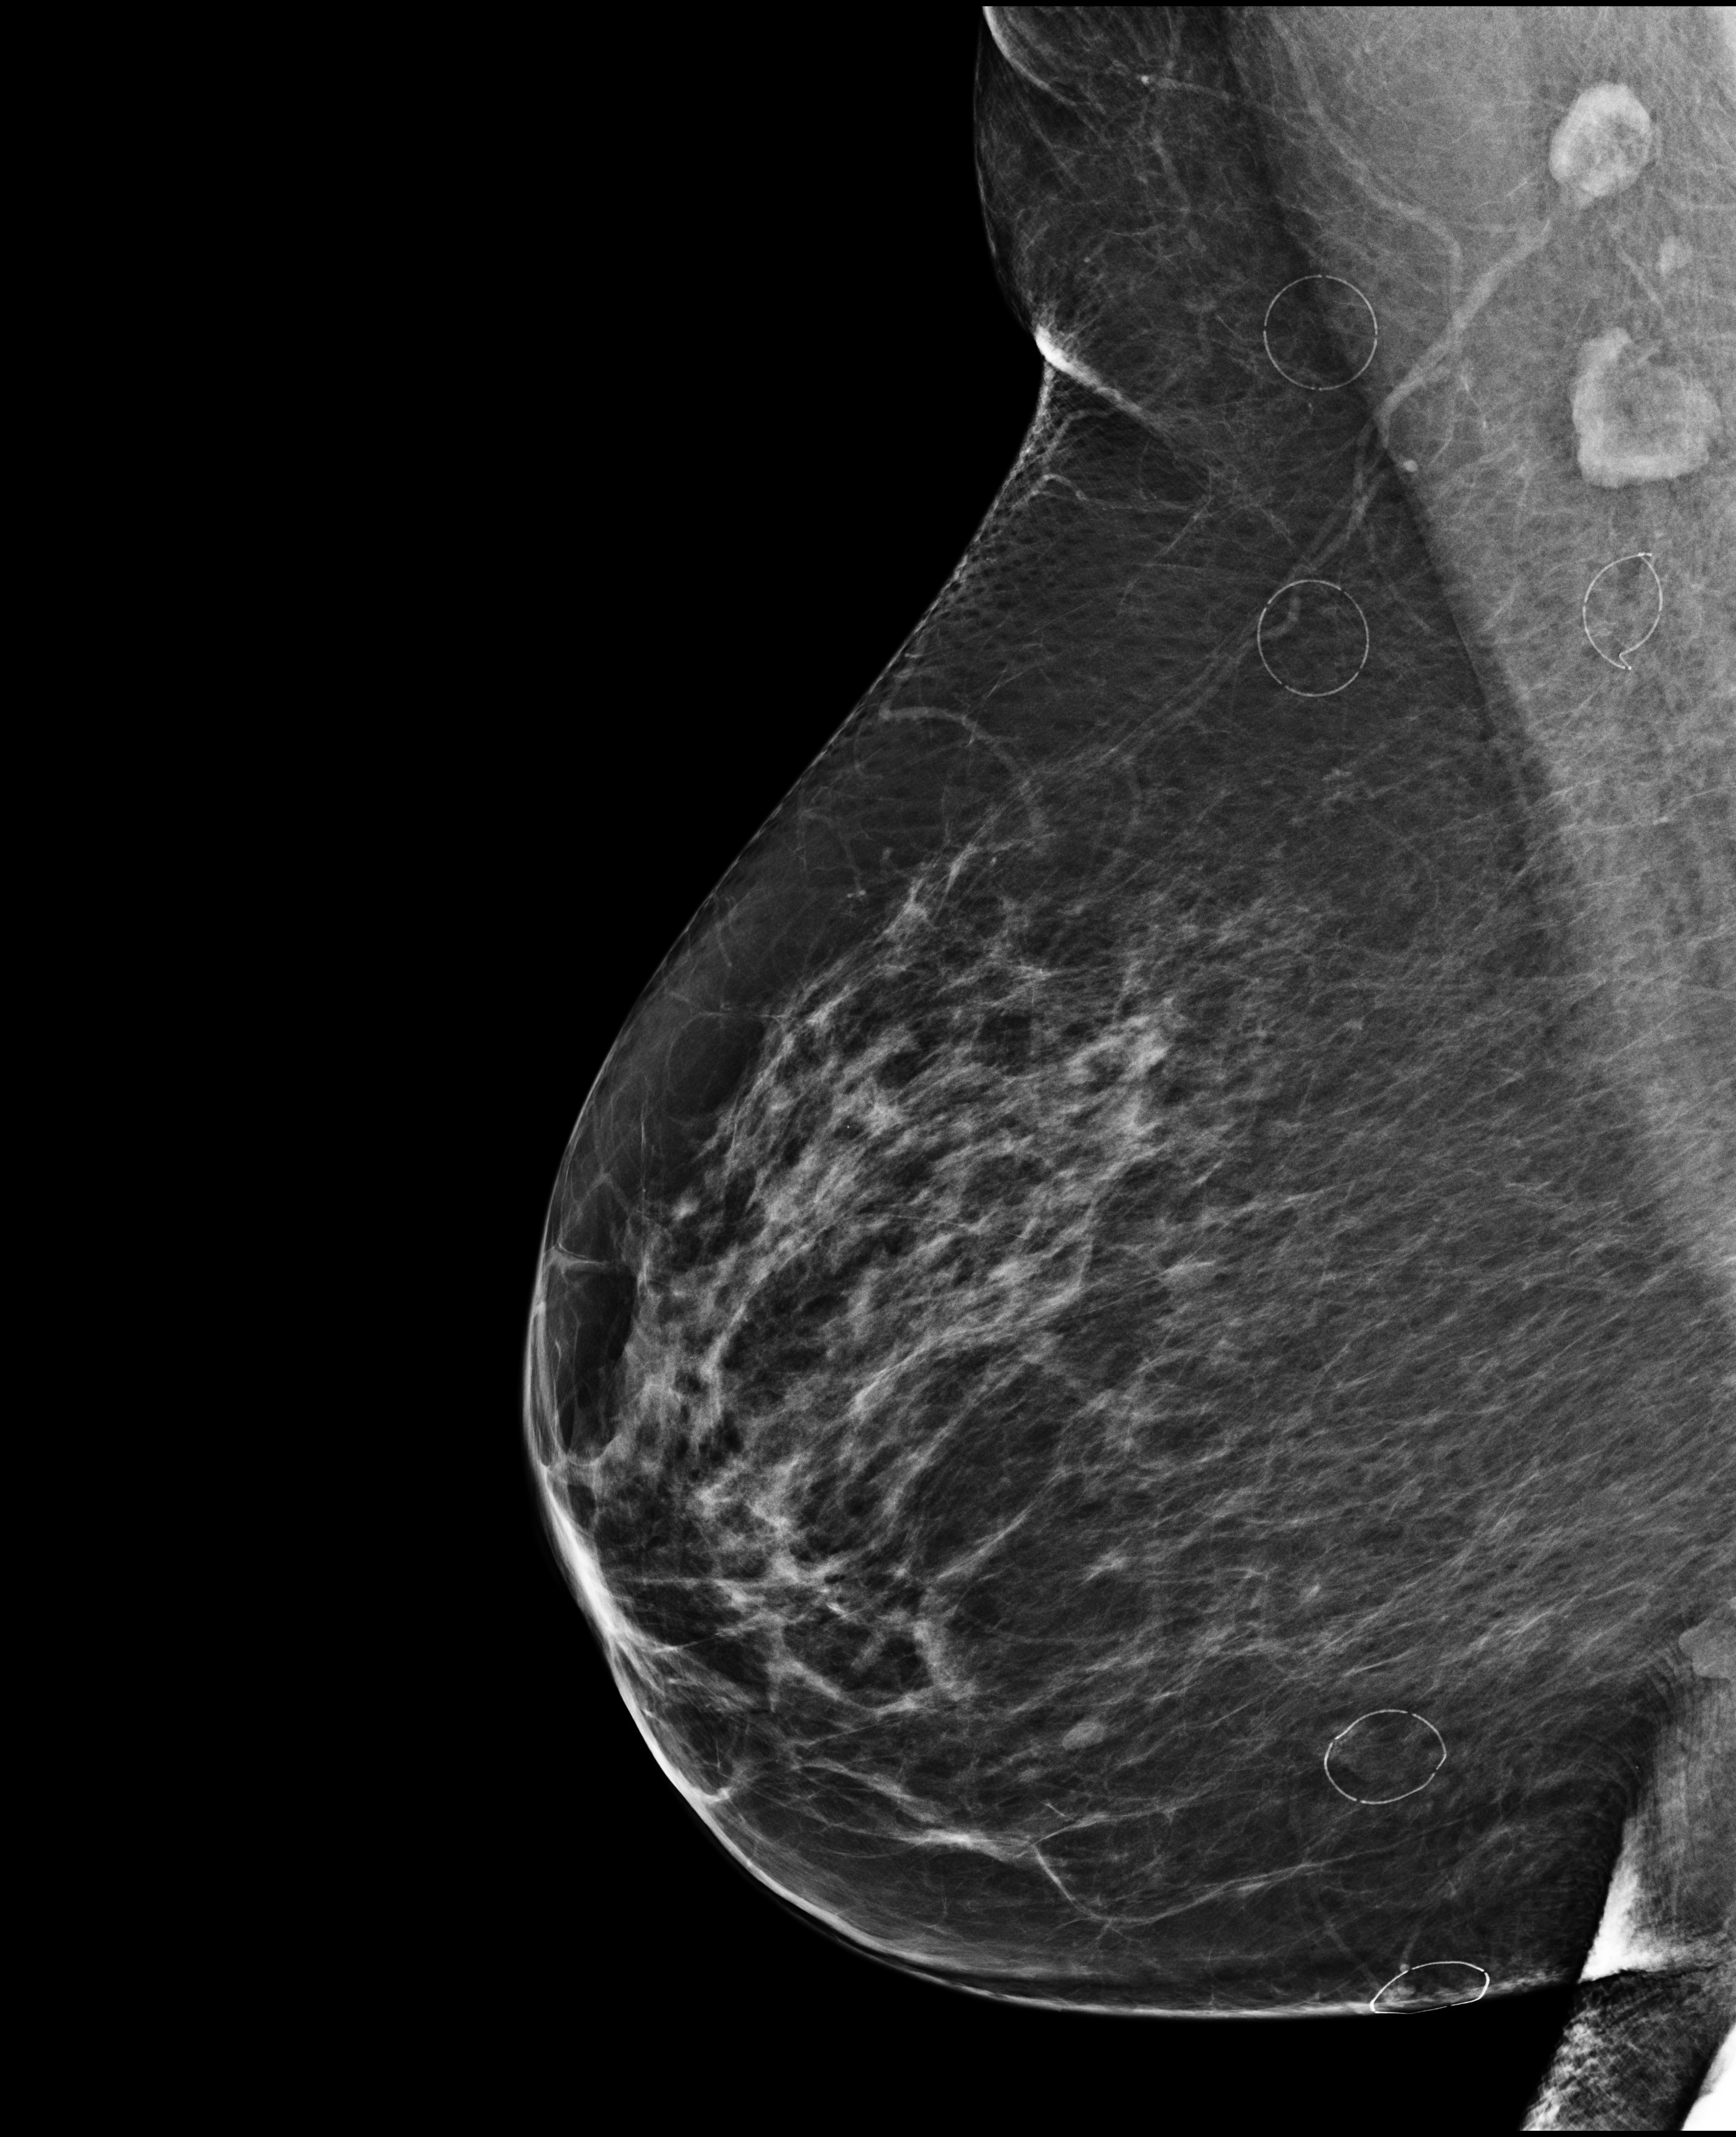
Screening examination, compressed breast thickness 70 mm. Patient: female, 67 years.
Image type: full-field digital mammogram. Breast: right. Projection: MLO view.